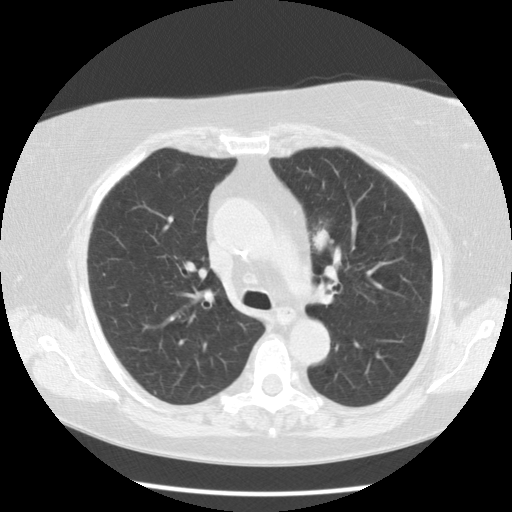
Chest CT (low-dose screening protocol), one axial image, second annual screen, lung window (W 1500 / L -600 HU), 2.5 mm slice thickness, standard (soft-tissue) reconstruction kernel (STANDARD), 512 × 512 image matrix. Female, age 67 years at enrolment. Former smoker at enrolment.
Expert-annotated lung lesion, bounding box <293,209,353,269> (left, top, right, bottom; pixels). Screening reader's record for this exam (one nodule recorded; not confirmed to be the boxed lesion): non-calcified nodule or mass ≥4 mm, left upper lobe, 20 × 18 mm, poorly defined margins, soft tissue attenuation, pre-existing on the prior screen: yes; interval growth: yes. Official screen result: positive, other. Participant outcome: lung cancer diagnosed 28 days after this screen — adenocarcinoma, NOS, left upper lobe, moderately differentiated (G2), stage IIA (AJCC 6th edition), 23 mm at pathology.